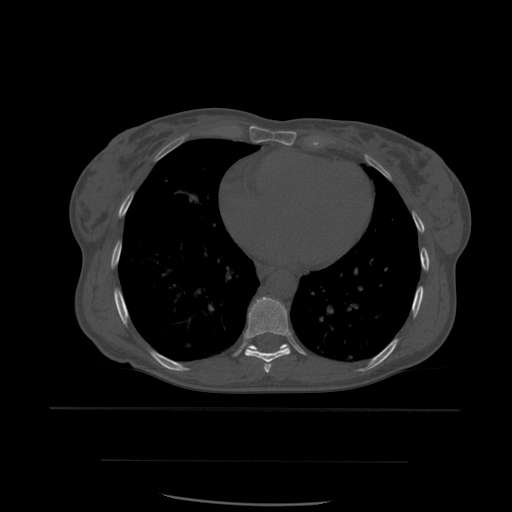
CT including the spine, one axial slice; bone window (W 1800 / L 400 HU); 1.25 mm slice thickness; 512 × 512 image matrix, field of view 392 × 392 mm. Patient age 48 years. Case-level facts recorded for this patient, not image findings: primary cancer: lung.
Annotated regions visible in this slice (semi-automatic segmentation, software-assisted and operator-edited):
- T7 vertebra: bounding box <265,364,271,373> (left, top, right, bottom; pixels)
- T8 vertebra: <244,297,291,372>
- T9 vertebra: <247,338,289,352>